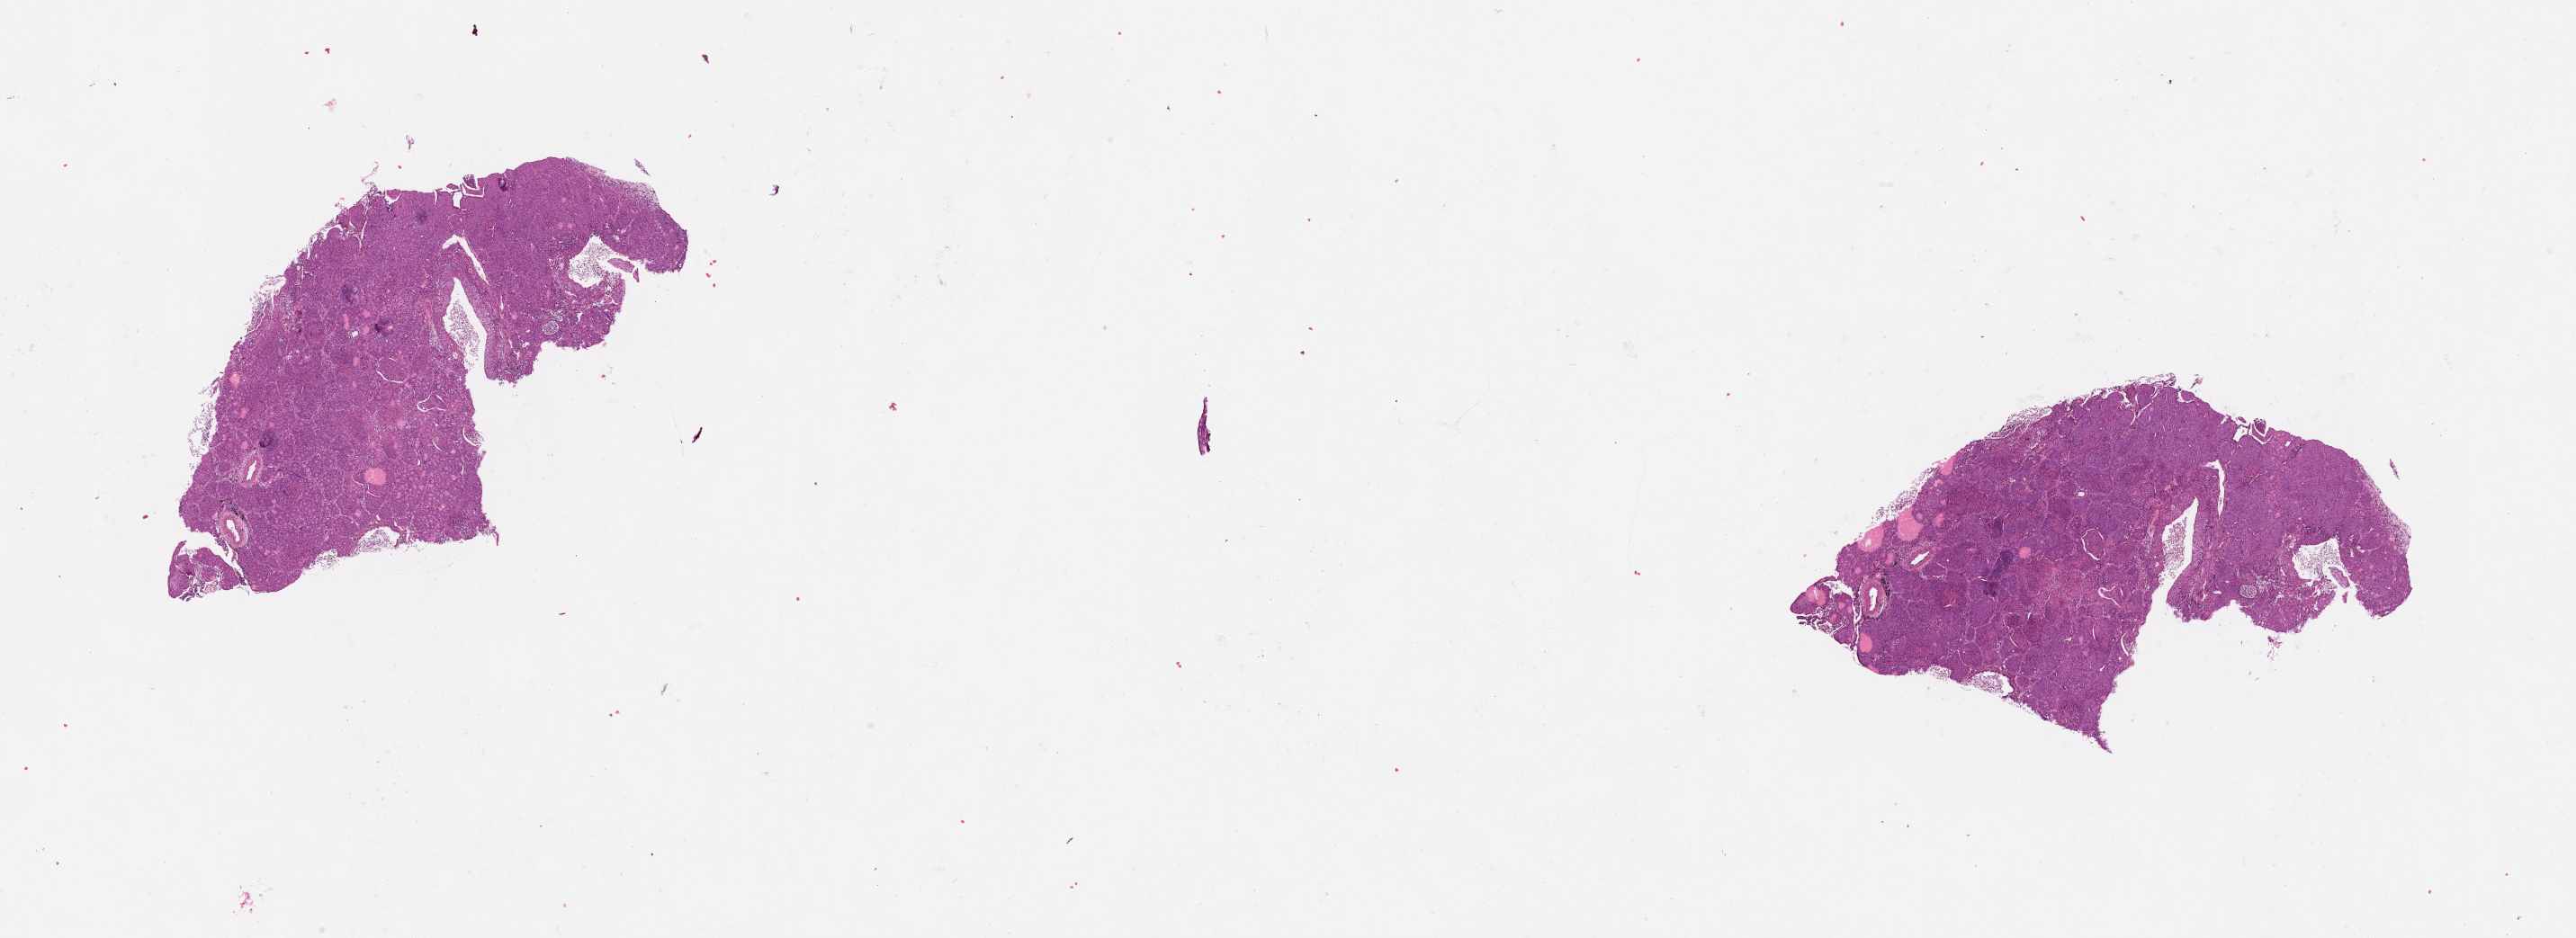
Hematoxylin and eosin (H&E) stained whole-slide image, shown as a low-resolution overview of the whole scanned area (about 23.1 x 8.4 mm). Lung, tumour tissue. 74-year-old female patient.
• patient diagnosis (cohort enrolment): squamous cell carcinoma (lung)